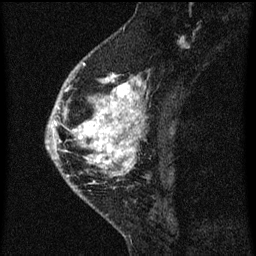
Breast MRI (dynamic contrast-enhanced), one sagittal slice. Slice 24 of 60 in the series (ordered by position). Dynamic contrast-enhanced series, image 2 of 3 at this slice position (ordered by acquisition). 1.5 T. TE 4.2 ms, TR 8 ms. 256 × 256 image matrix. Patient: female, 46 years.
Annotated regions visible in this slice (semi-automatic segmentation, software-assisted and operator-edited):
- analysis volume of interest (the breast-tissue region the enhancement analysis was run in; not a lesion): bounding box <59,68,145,195> (left, top, right, bottom; pixels)
- tumour enhancement mask (voxels above the 70 % enhancement threshold inside the analysis volume of interest): <59,74,145,185>